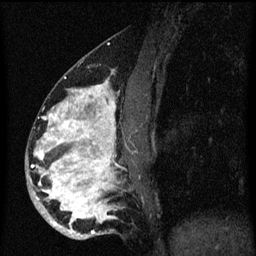
Breast MRI (dynamic contrast-enhanced), one sagittal slice. Position 27 of 60 along the scan axis. Dynamic contrast-enhanced series, image 2 of 3 at this slice position (ordered by acquisition). 1.5 T. TE 4.2 ms, TR 8.4 ms. 2 mm slice thickness. 256 × 256 image matrix, field of view 180 × 180 mm. Patient: female, 34 years. From the clinical record (not read from this slice): setting: breast cancer imaged before/during neoadjuvant chemotherapy; receptor status: HR-positive, HER2-negative.
Structures marked on this image (semi-automatically segmented with operator editing):
- analysis volume of interest (the breast-tissue region the enhancement analysis was run in; not a lesion): bounding box (x1, y1, x2, y2) in pixels: (26, 58, 141, 241)
- tumour enhancement mask (voxels above the 70 % enhancement threshold inside the analysis volume of interest): (34, 80, 117, 235)